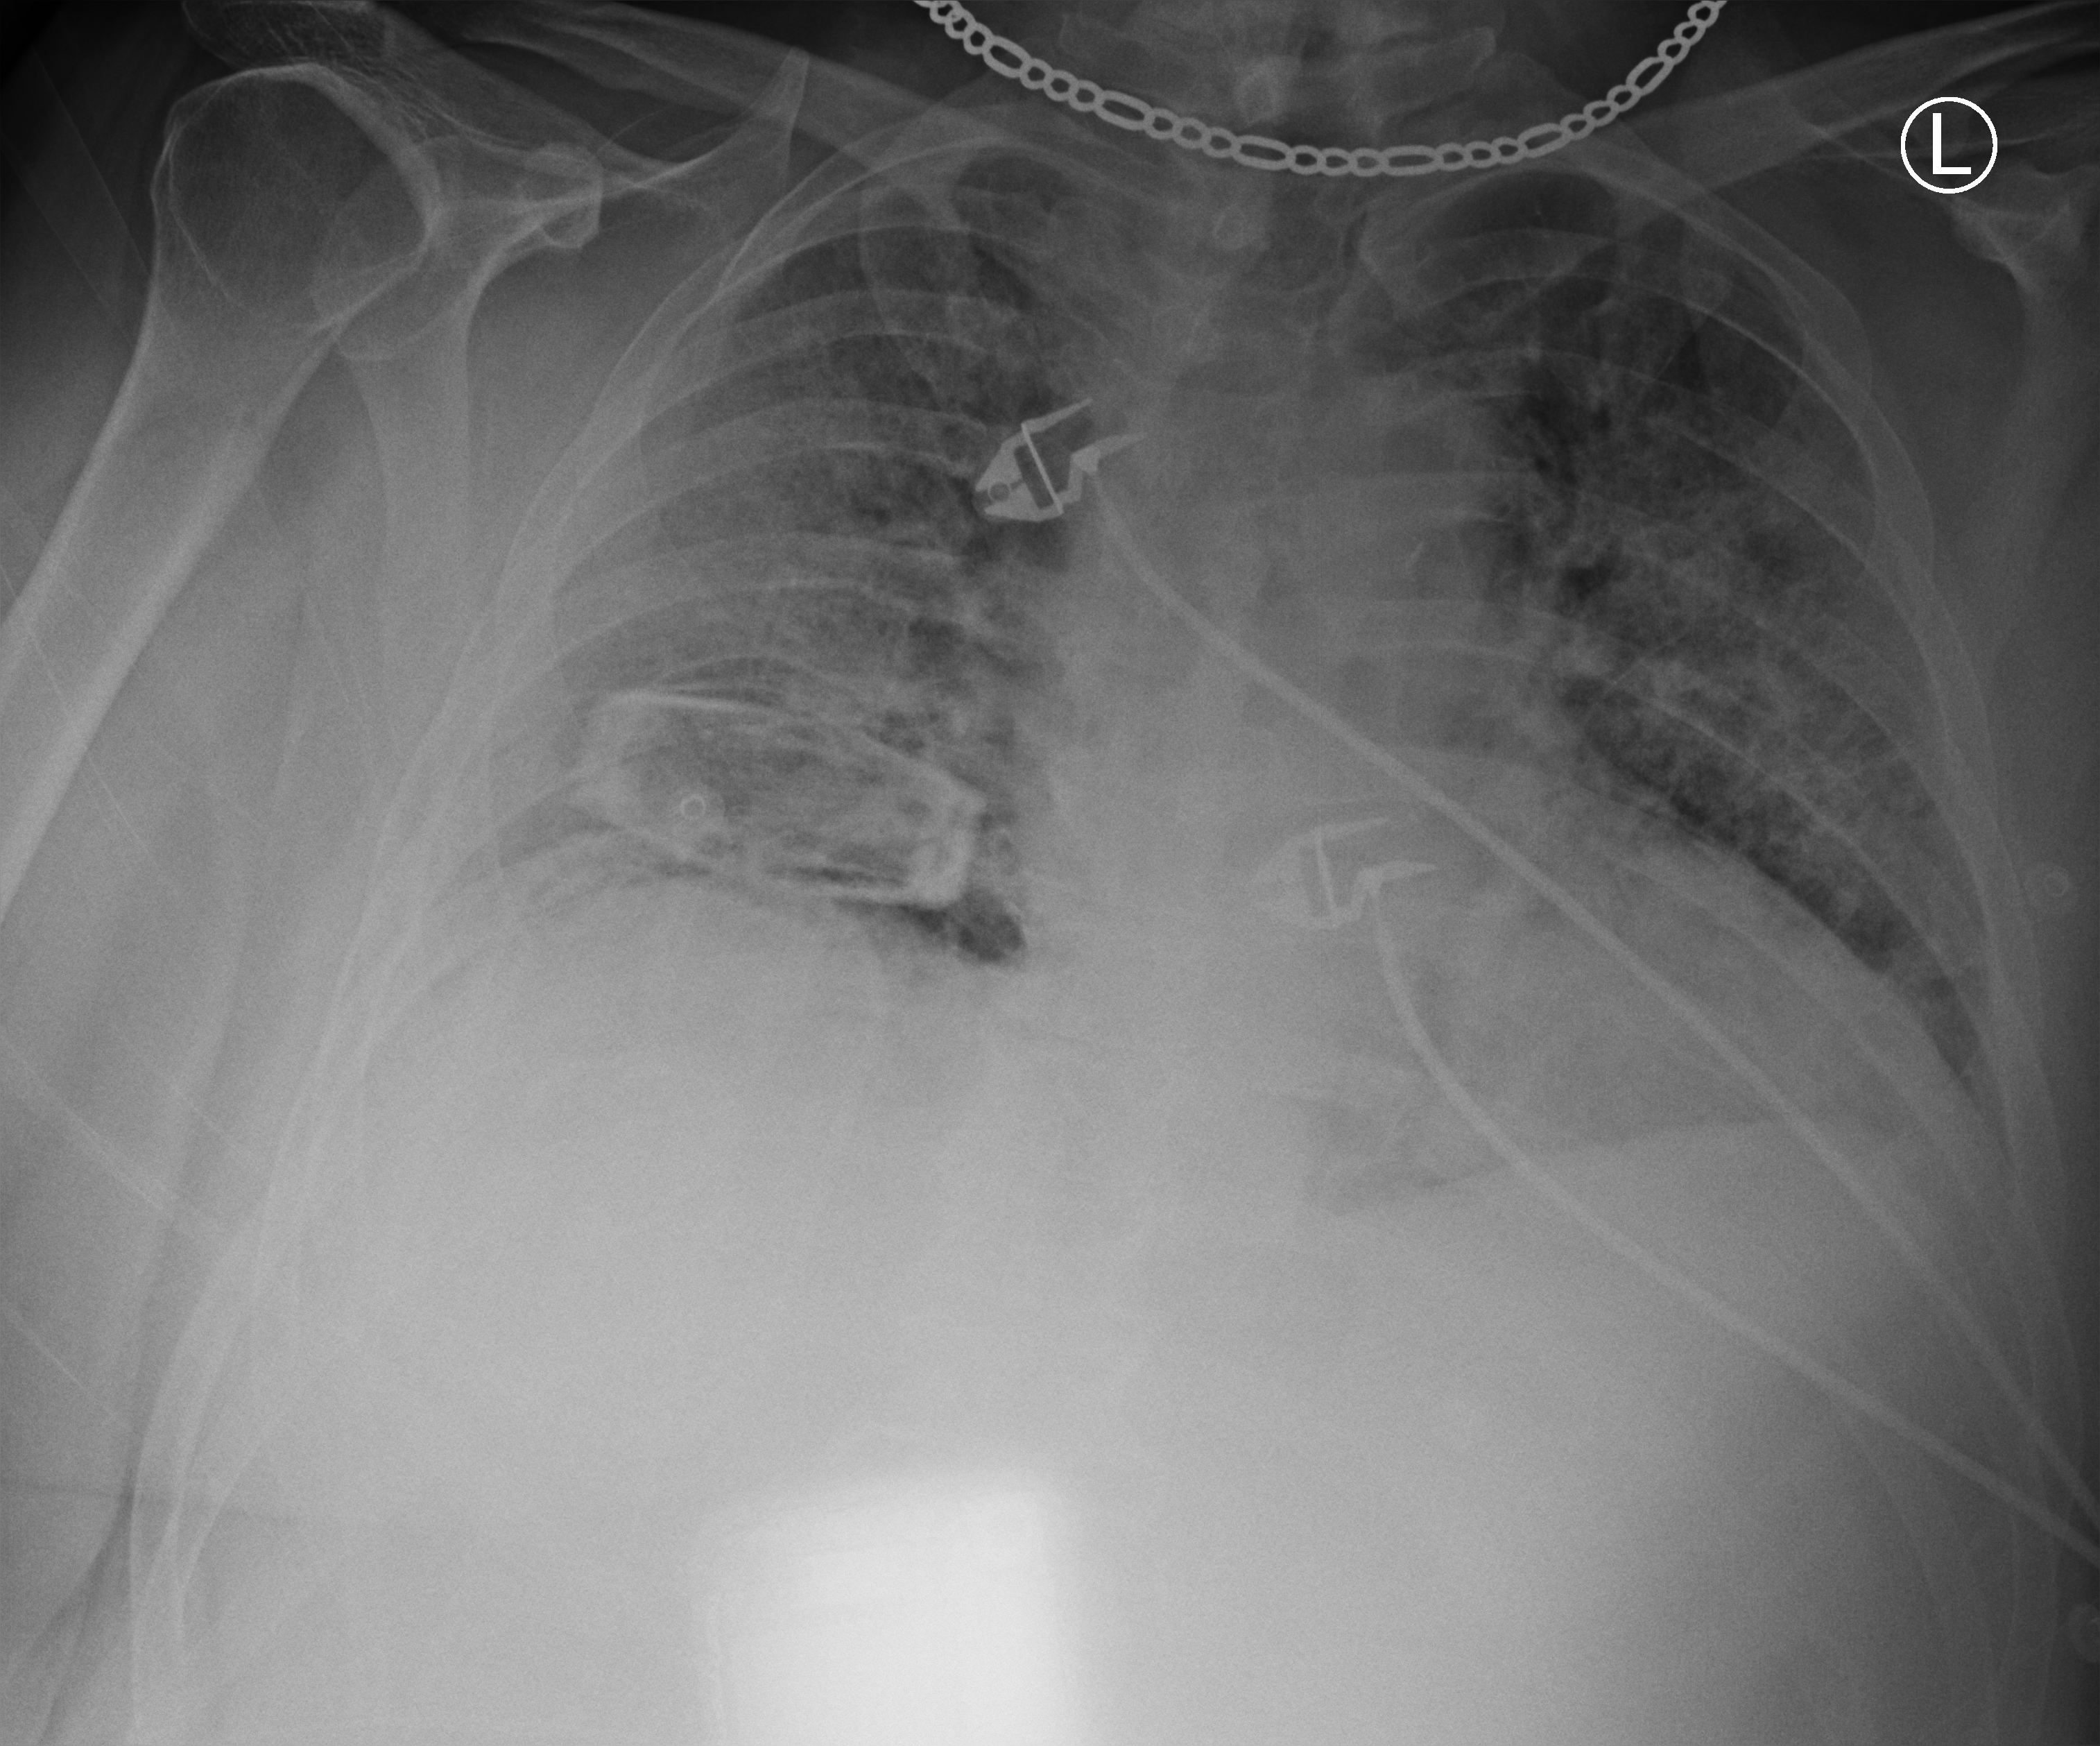
Portable chest radiograph, anteroposterior (AP) projection. Patient hospitalised with COVID-19; male, aged 60–74 years.
Admission-level facts for this patient (not findings on this image; timing relative to this image not recorded):
- admitted to intensive care during this hospital stay: no